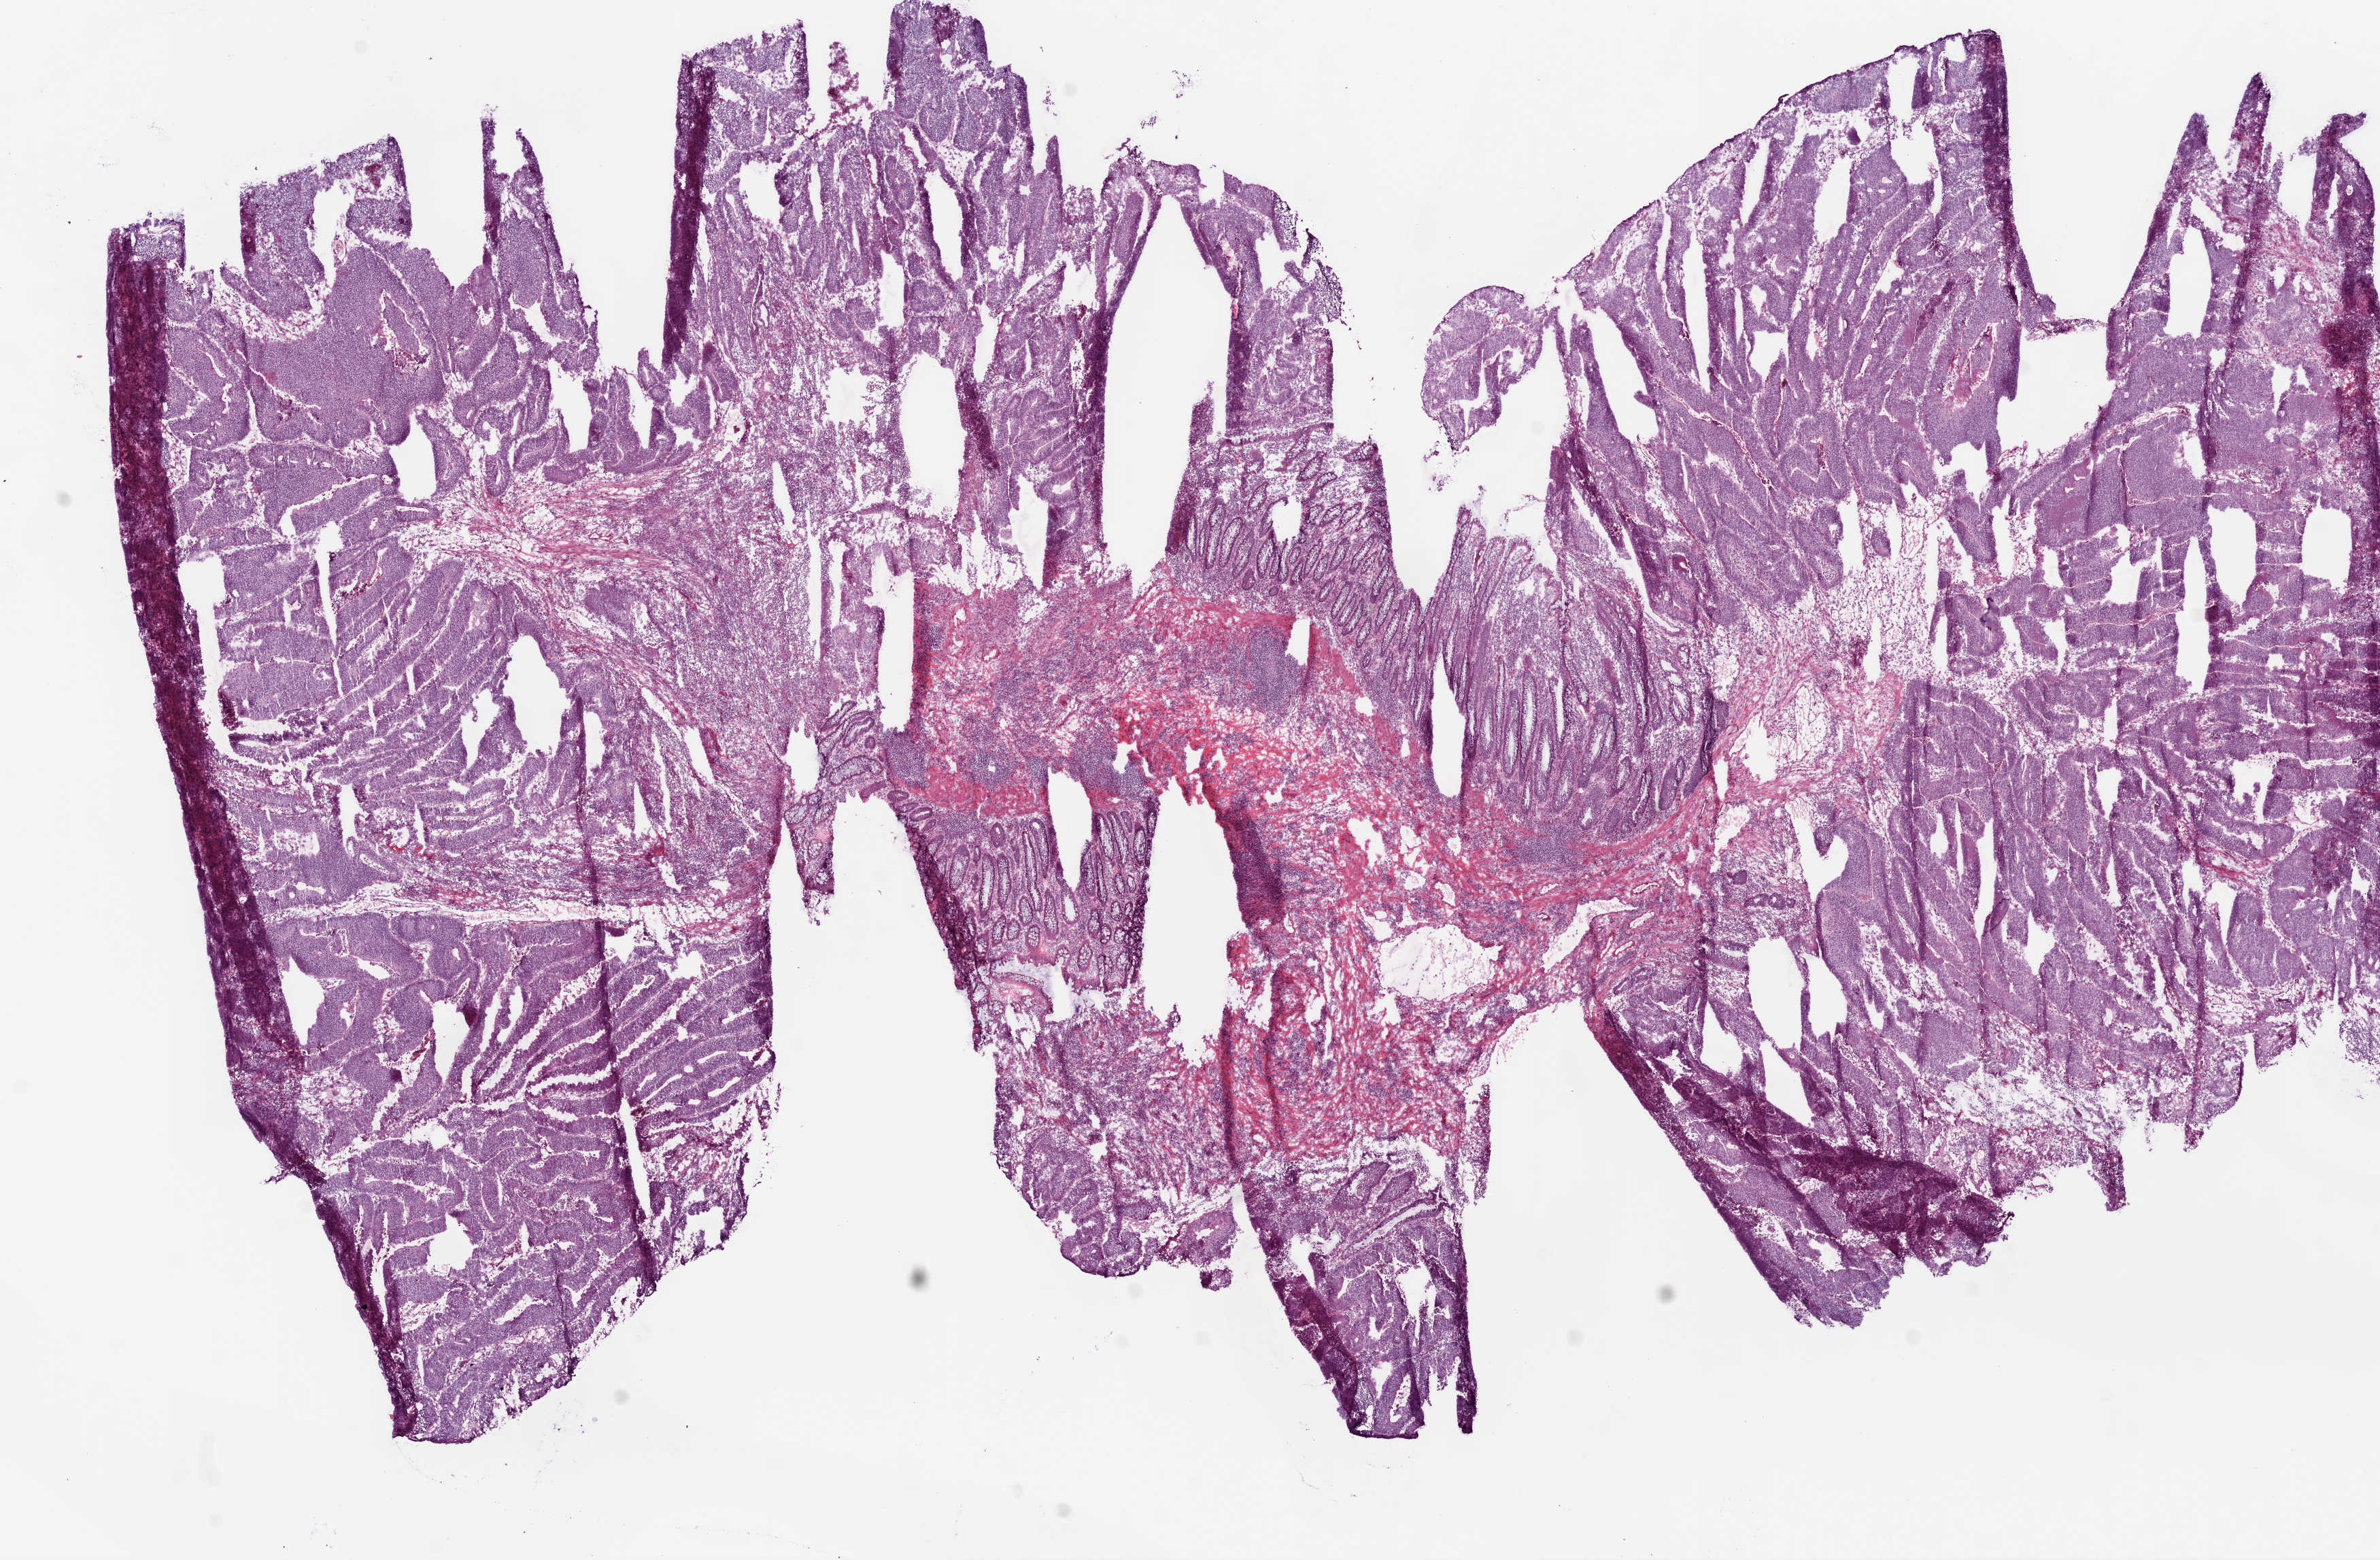
Digitized Hematoxylin and eosin (H&E) stained tissue section (whole slide), shown as a low-resolution overview of the whole scanned area (about 14.0 x 9.2 mm); frozen section; rectum, primary tumour sample. Male, age 67 years at initial diagnosis. Slide review estimates, as recorded: tumour cells 70%, tumour nuclei 80%, normal cells 10%, stromal cells 10%, necrosis 10%.
Lymph nodes positive (case pathology): 0 of 22 examined. AJCC pathologic stage: I (5th edition). Pathologic diagnosis: Adenocarcinoma, NOS (rectosigmoid junction).